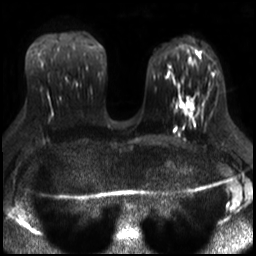
Breast MRI, one axial slice. Slice 16 of 30 in the series (ordered by position). Diffusion-weighted series; image 2 of 4 stored at this slice position (different b-values; order by instance number). 3 T. 256 × 256 image matrix. Female patient.
Outlined on this slice (manually delineated by an expert):
- tumour on diffusion-weighted imaging: bounding box (x1, y1, x2, y2) in pixels: (184, 97, 194, 111)